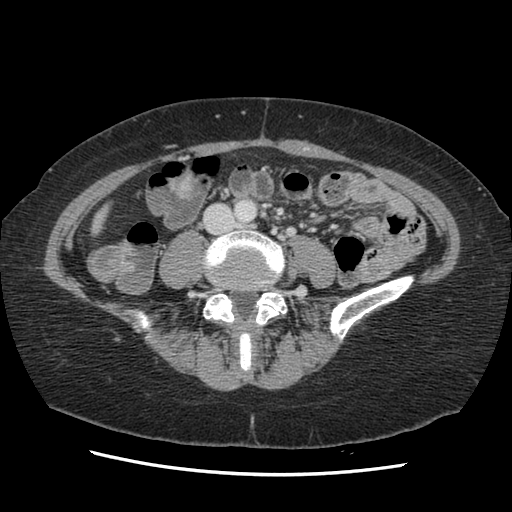
Contrast-enhanced abdominal CT, one axial slice. Slice 12 of 141 in the series (ordered by position). 120 kVp. Soft-tissue window (W 400 / L 40 HU). 512 × 512 image matrix. Female patient, age 61 years. From the clinical record (not read from this slice): diagnosis: colorectal cancer liver metastases, imaged before liver resection; multiple liver metastases: no; largest metastasis: 2.4 cm; disease in both lobes: no.
Outlined on this slice (manually delineated by an expert):
- liver: bounding box (x1, y1, x2, y2) in pixels: (95, 207, 107, 232)
- planned liver remnant (the part of the liver to remain after resection): (95, 208, 107, 232)